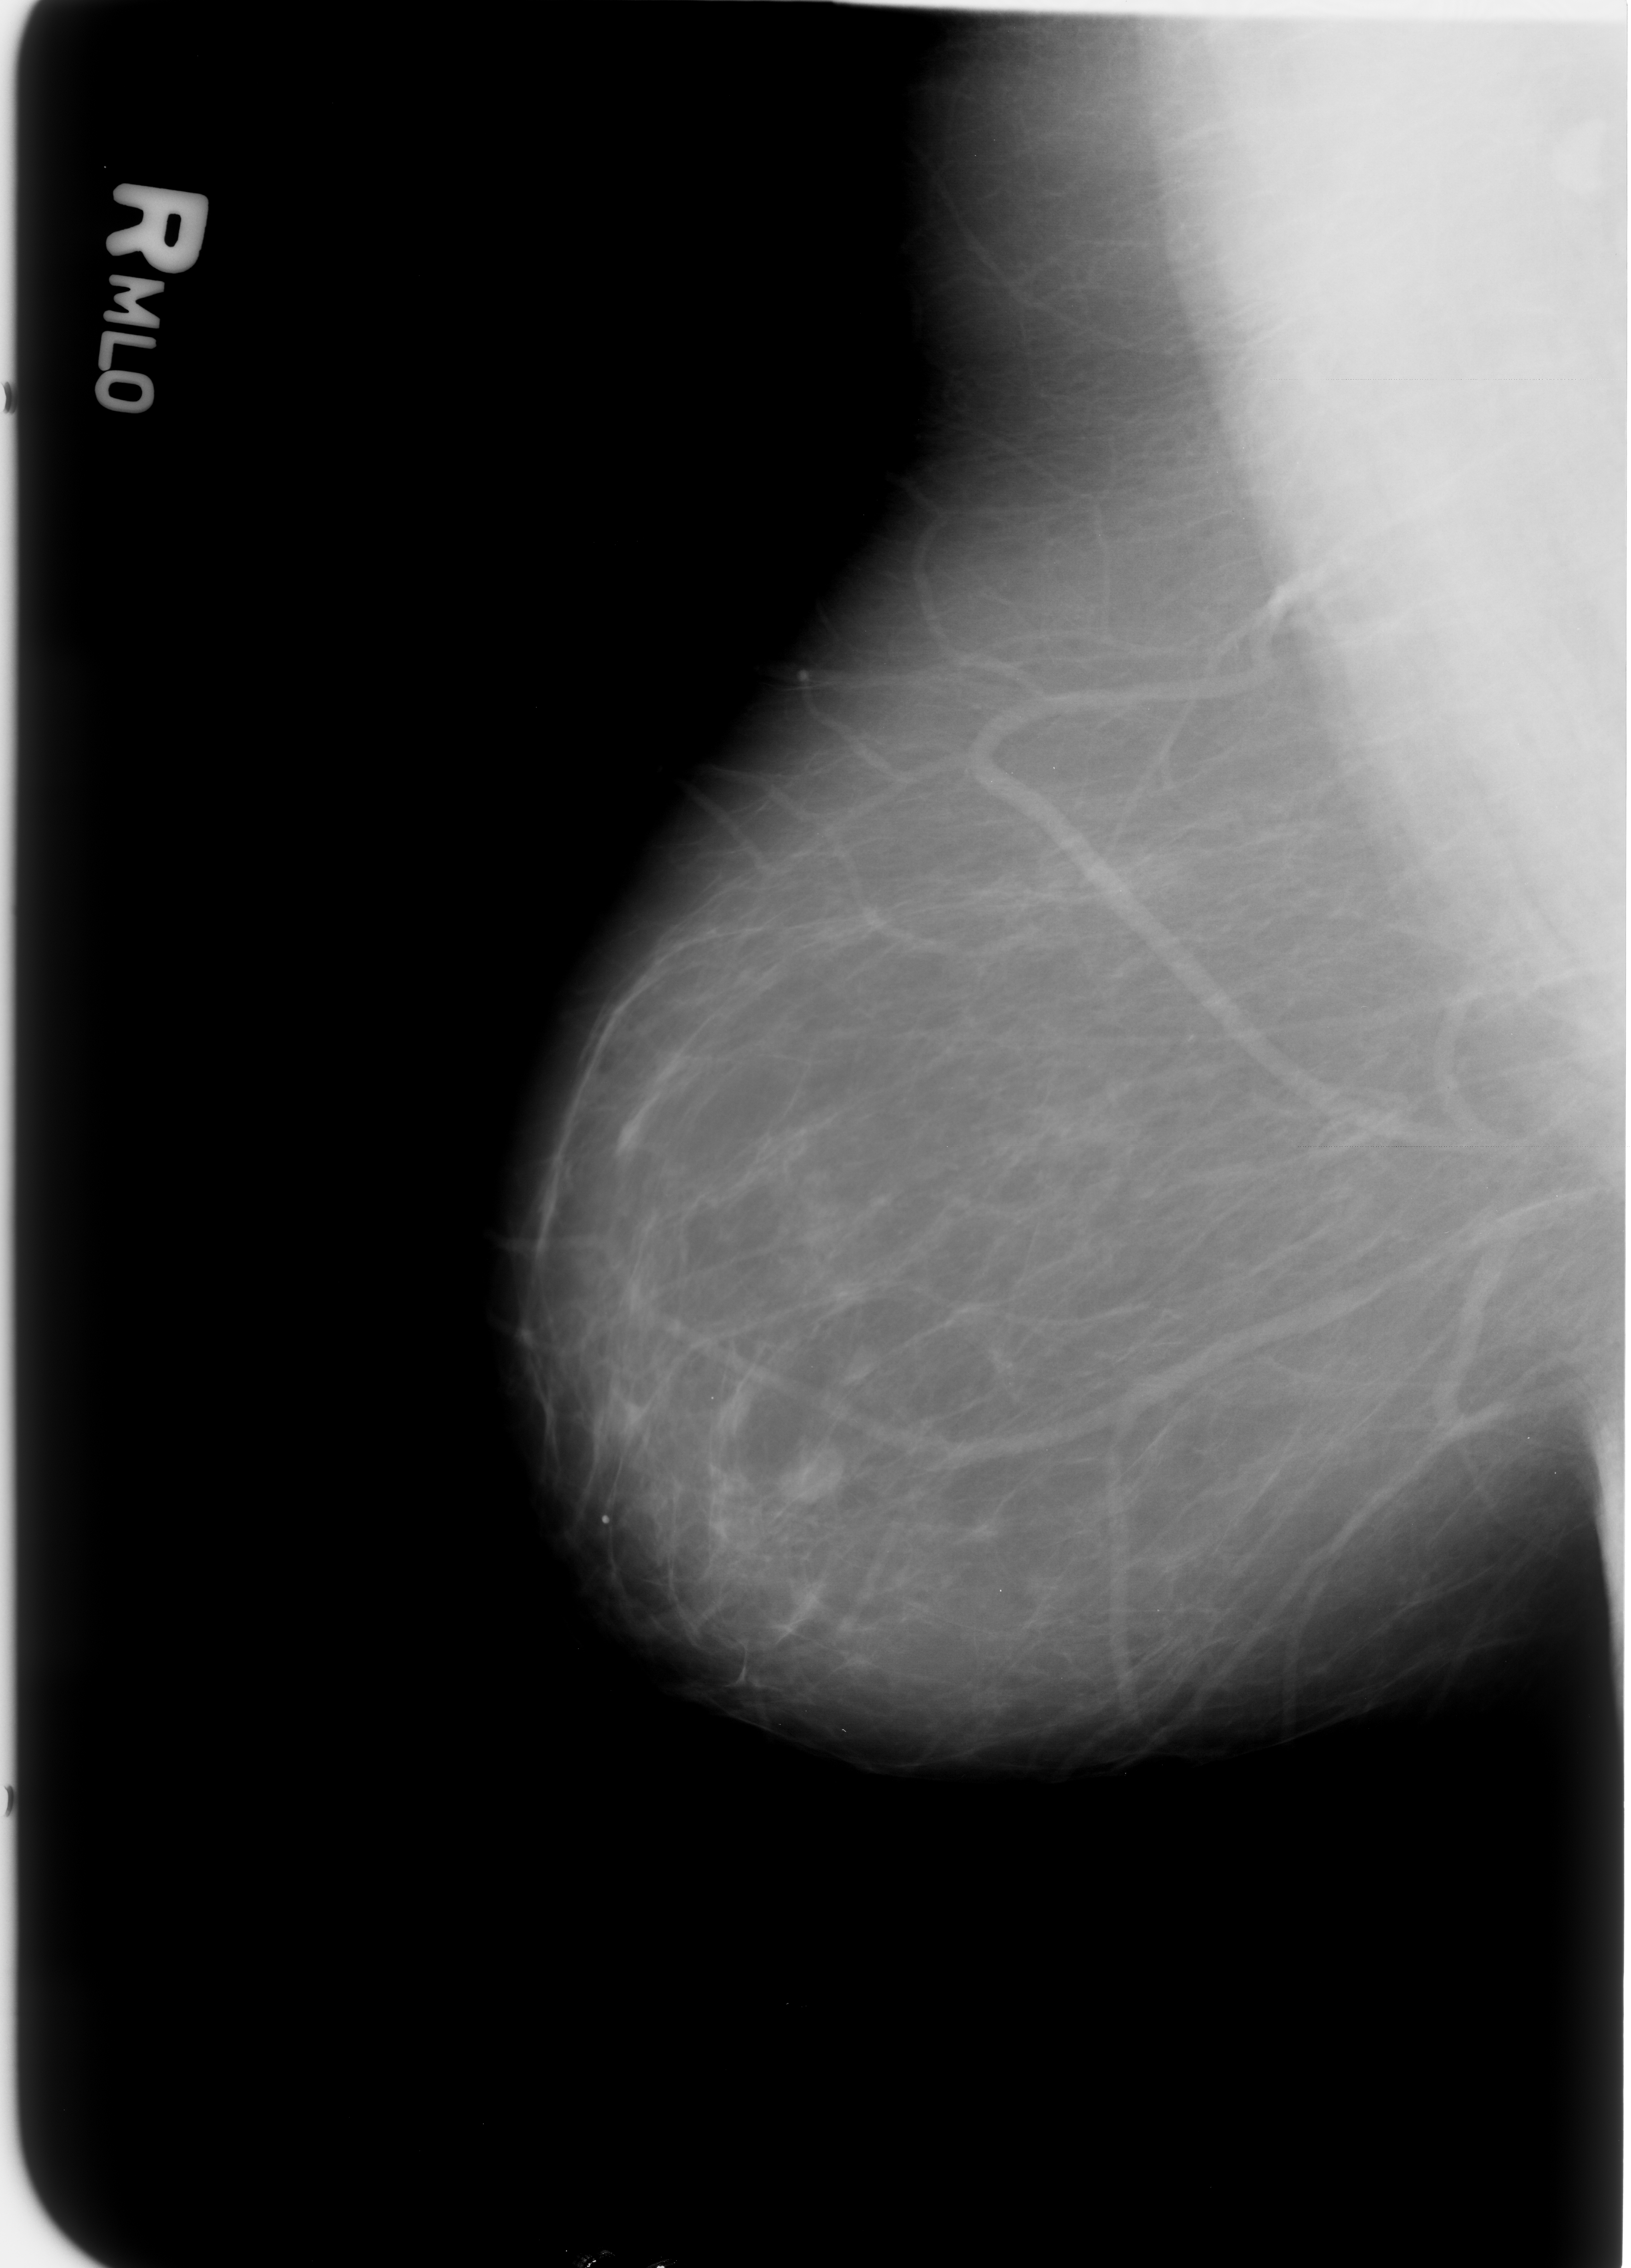
Mammogram (digitized film), right breast, MLO view, BI-RADS breast density category 1 (scale 1–4).
Marked findings (only marked abnormalities are described; nothing is implied about the rest of the image): mass, shape lobulated, margins circumscribed / ill defined; BI-RADS assessment category 4; pathology (as recorded): benign.